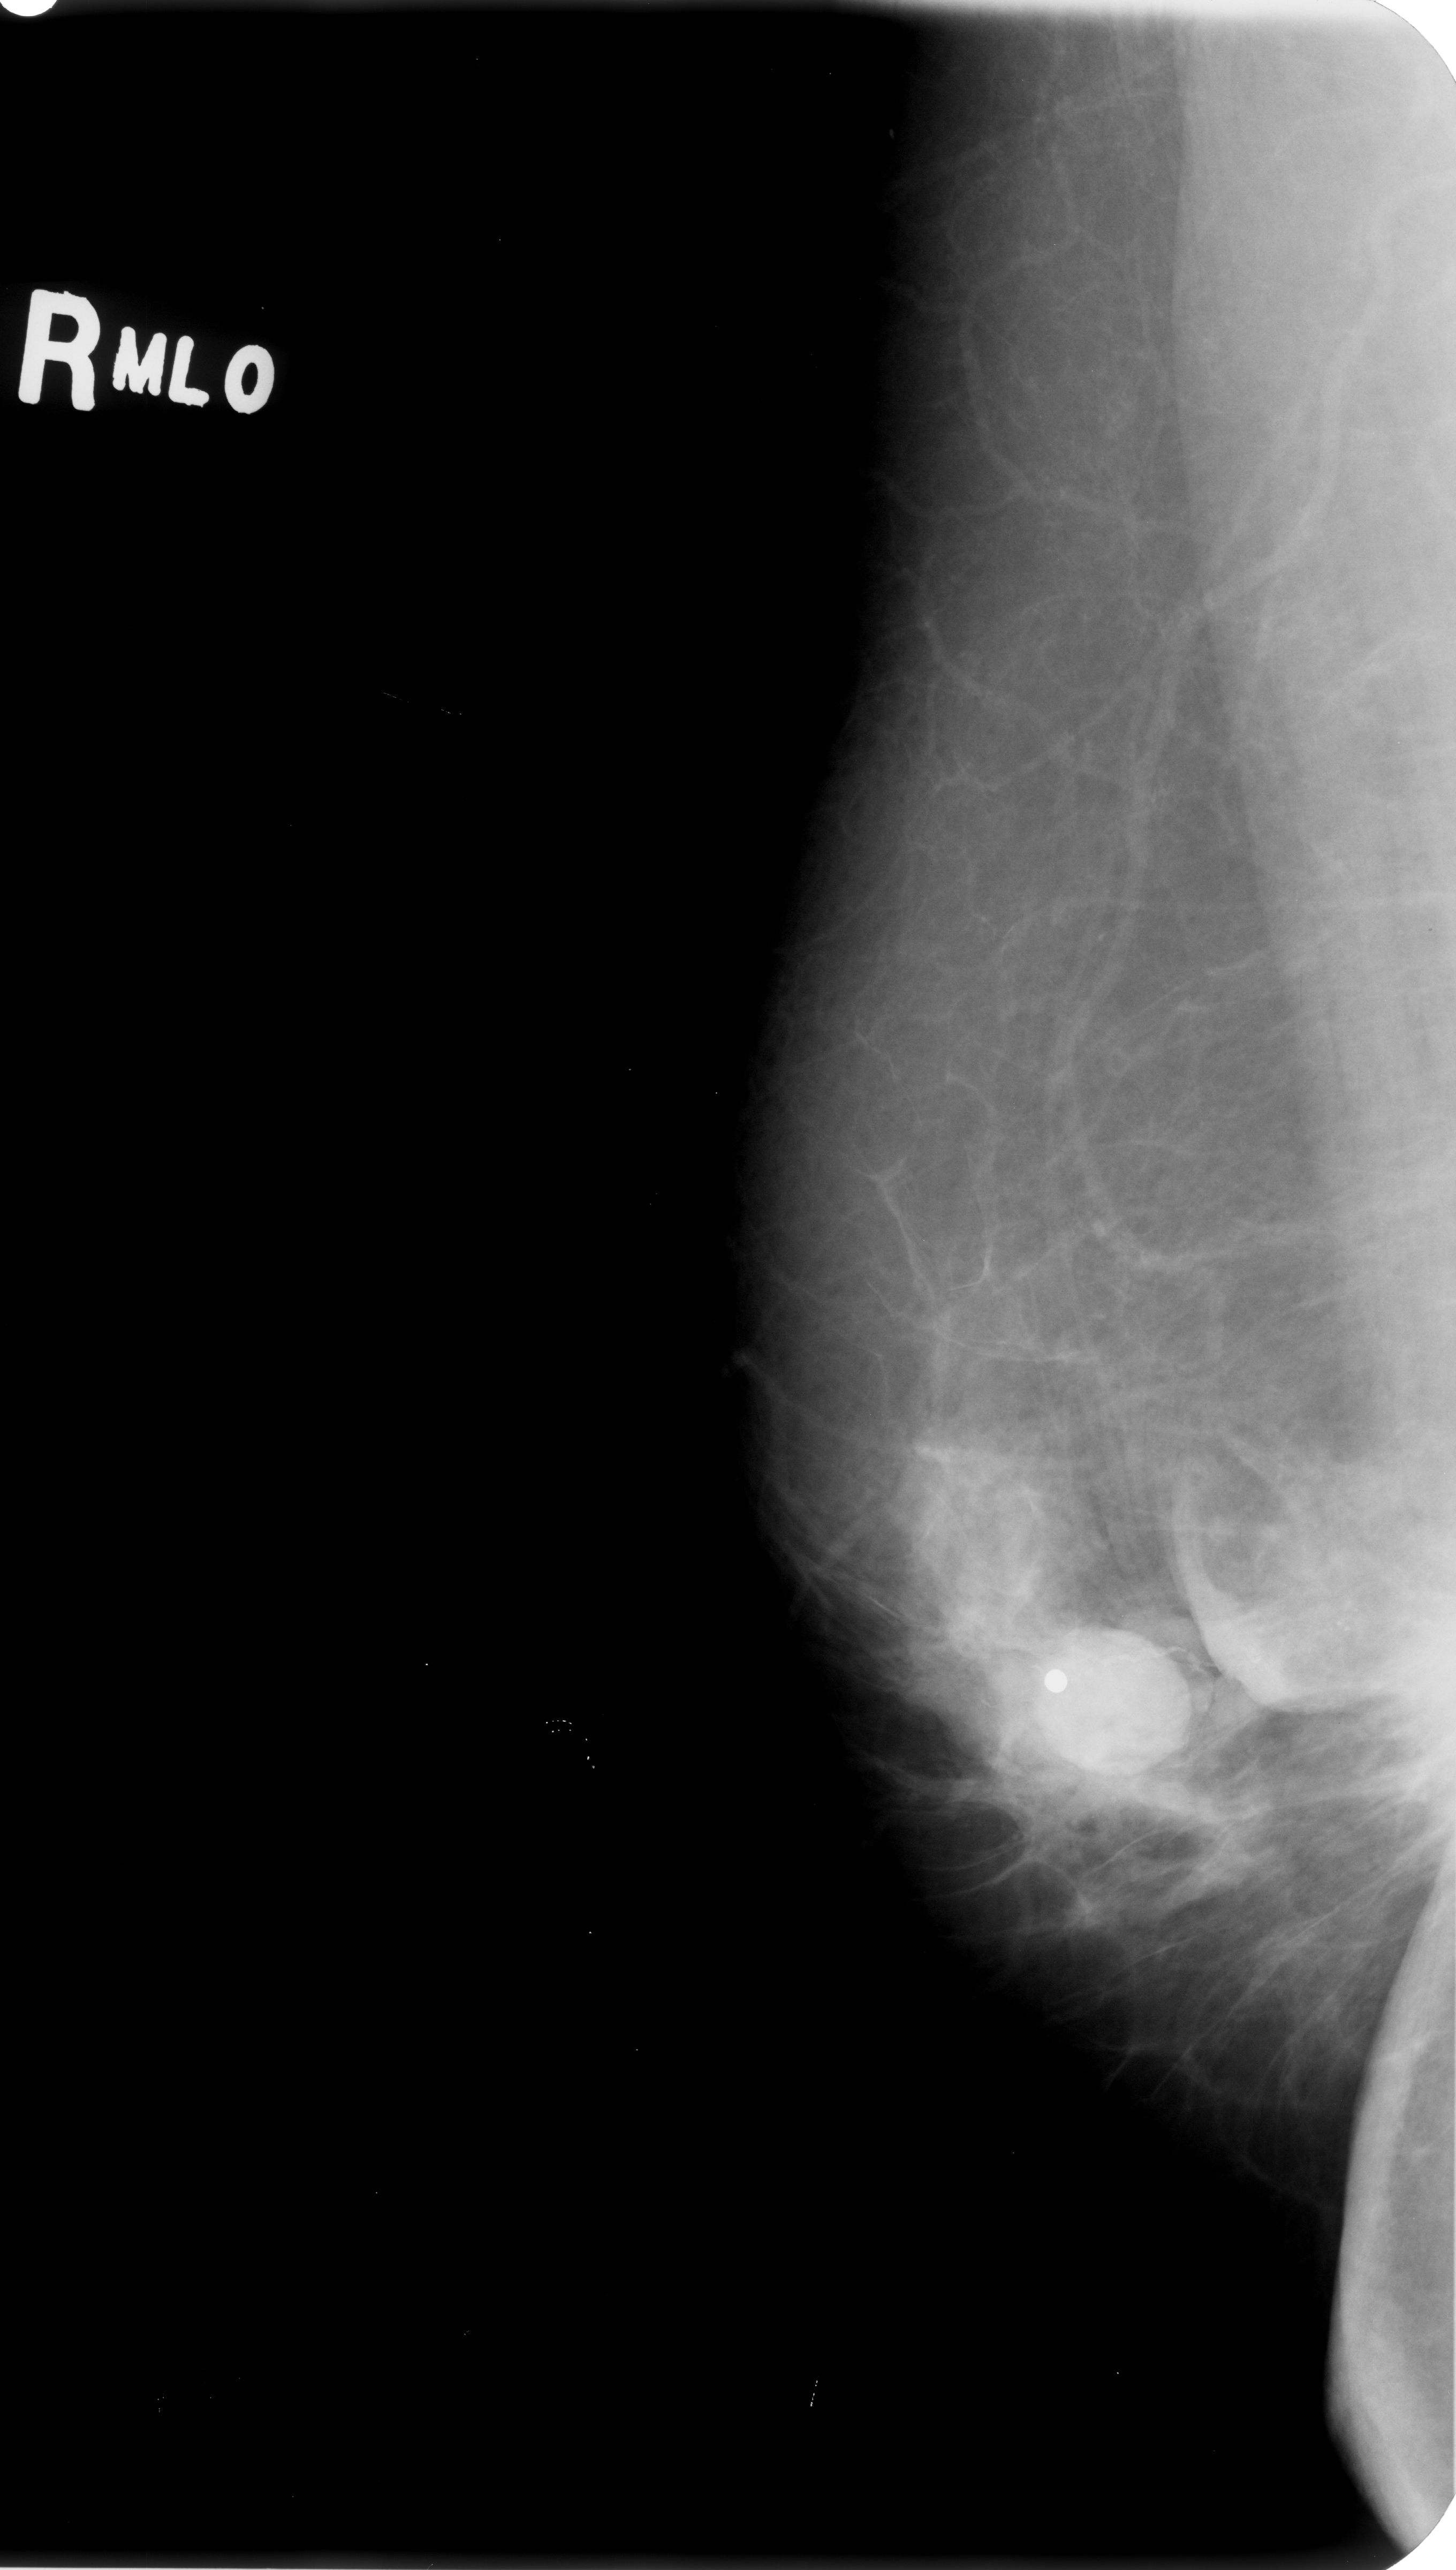
Mammogram (digitized film); right breast; MLO view; breast composition: scattered fibroglandular densities (BI-RADS density category 2 of 4).
Marked abnormality: calcifications, morphology pleomorphic / fine linear branching, distribution clustered / linear; BI-RADS assessment category 5; pathology (as recorded): malignant.